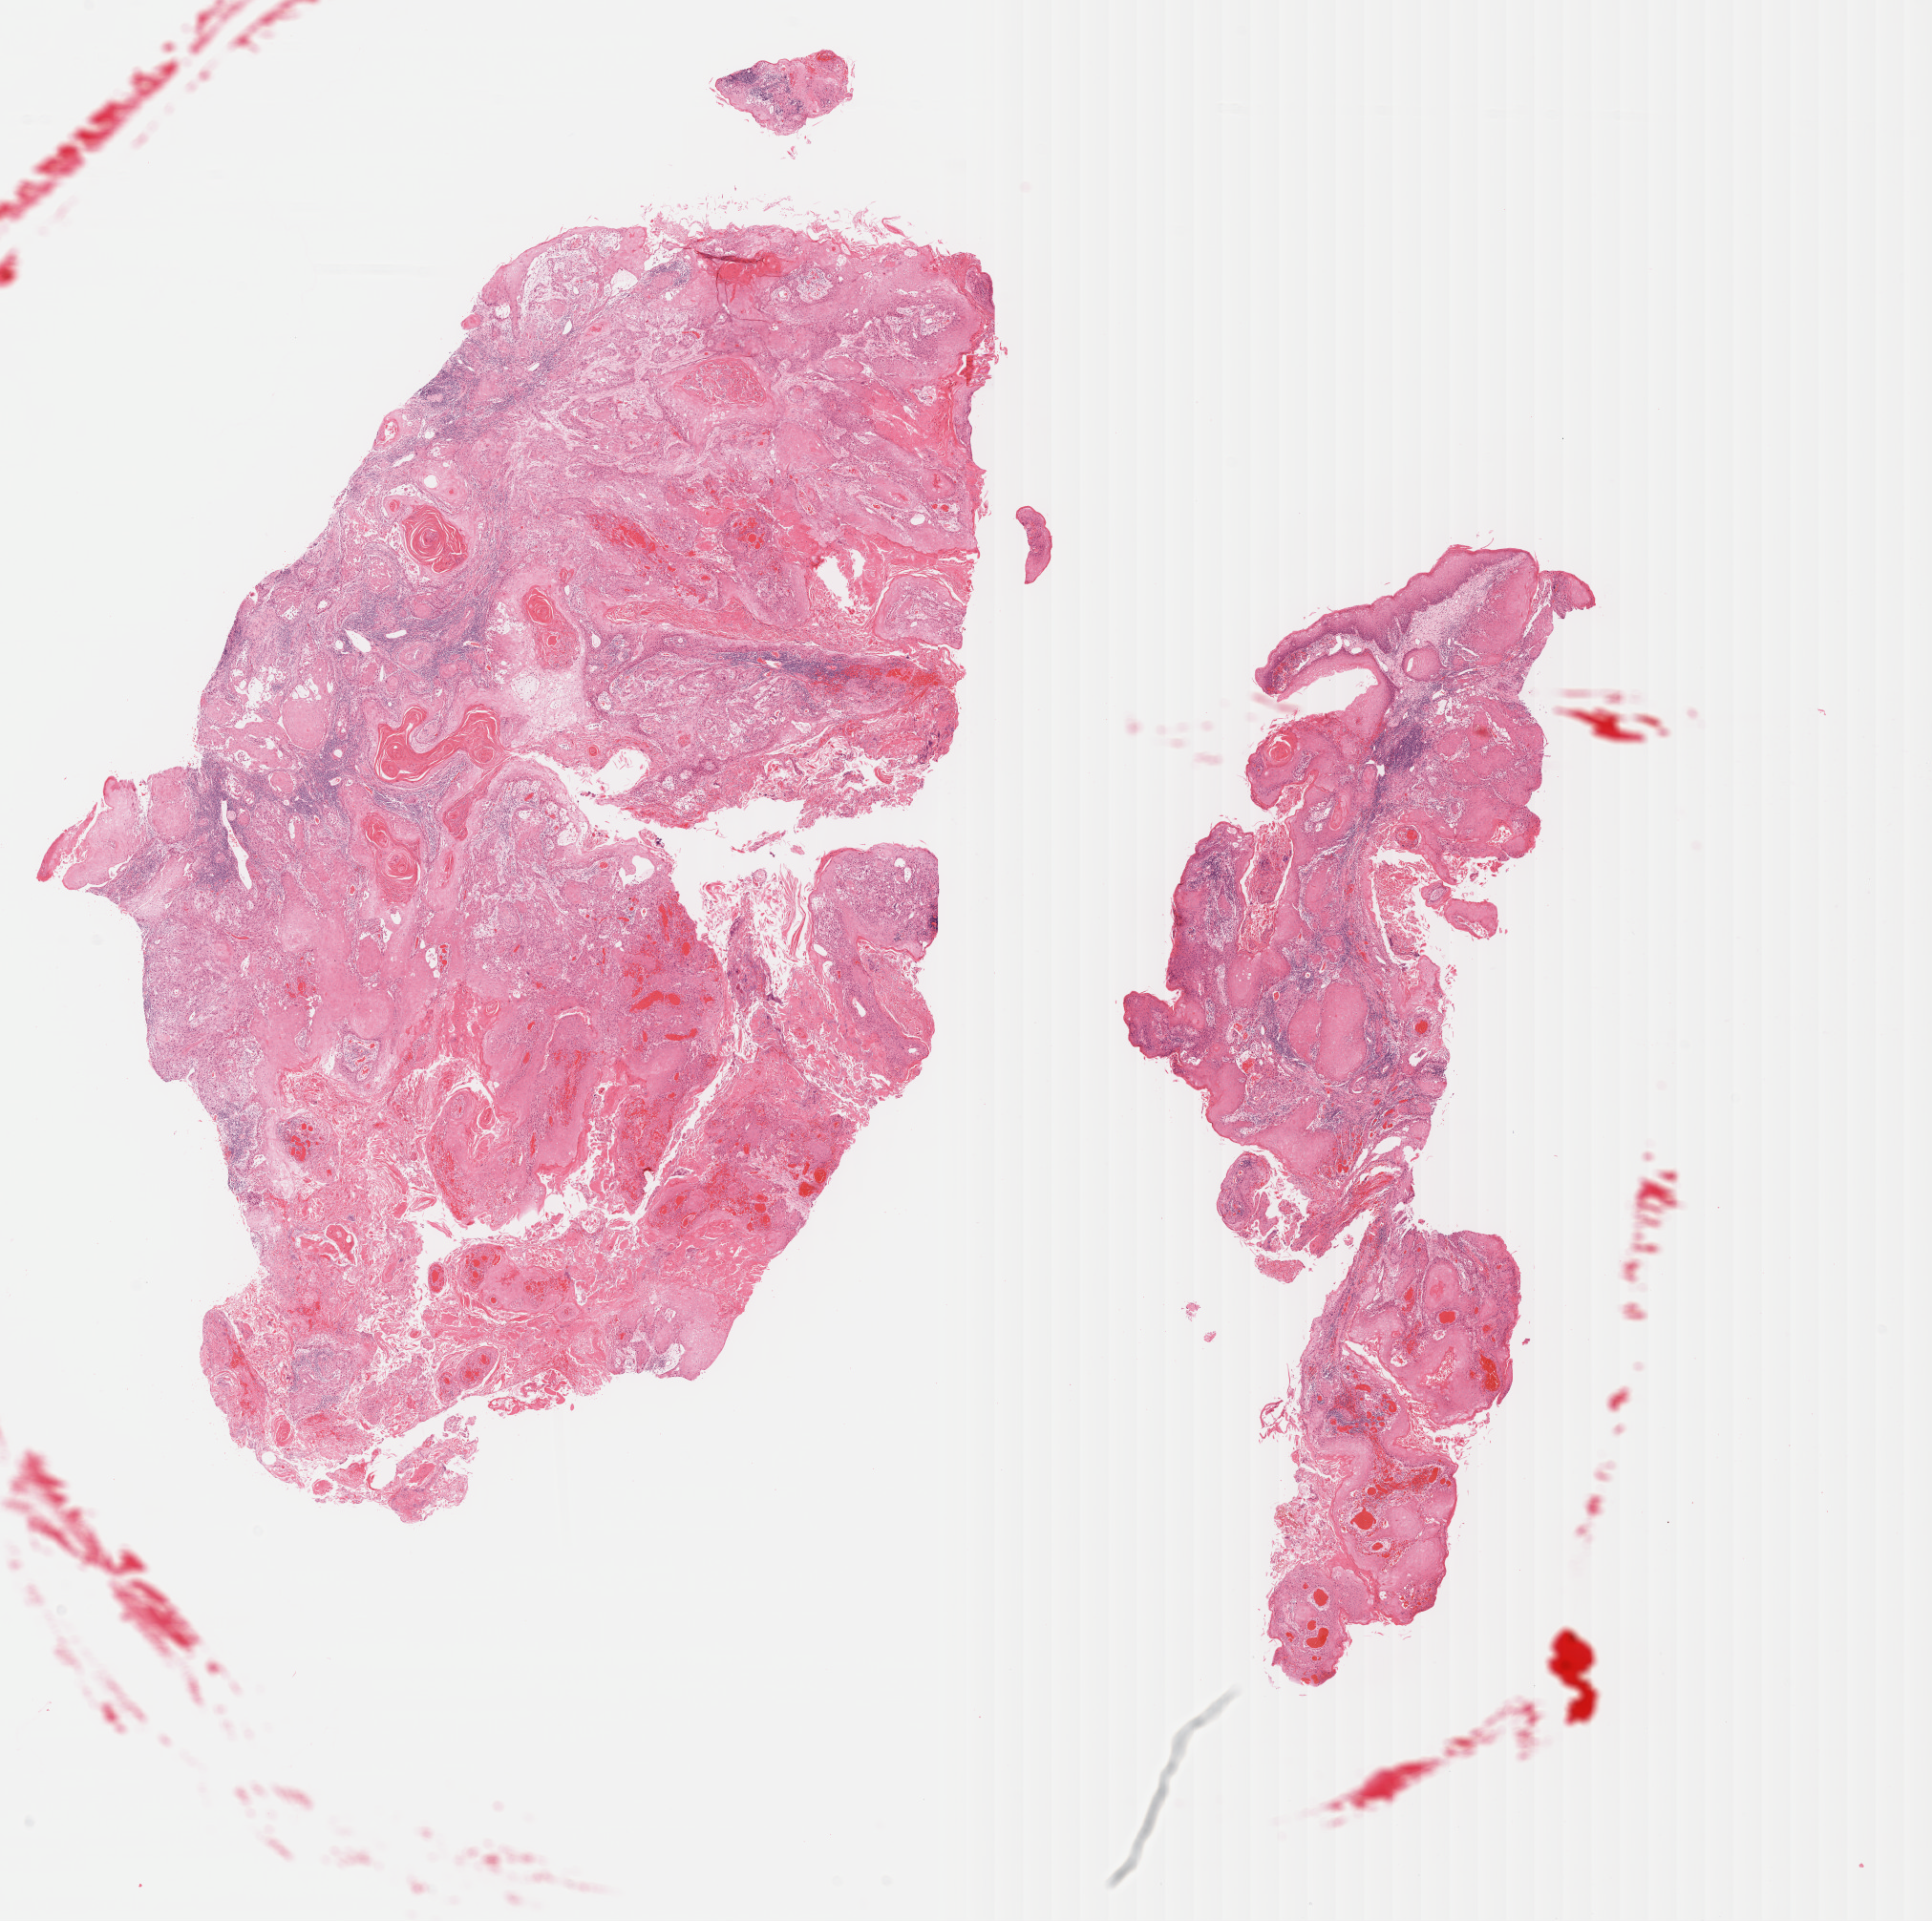
Digitized H&E tissue section (whole slide) — a low-resolution overview of the entire scanned area, about 15.9 x 15.8 mm. Formalin-fixed paraffin-embedded (FFPE) diagnostic section. Primary tumour sample from the head and neck. Female patient; age at initial diagnosis 67 years. Histologic grade: G2 (moderately differentiated).
Pathologic diagnosis: Squamous cell carcinoma, keratinizing, NOS (tongue, NOS). AJCC pathologic stage: III (7th edition).